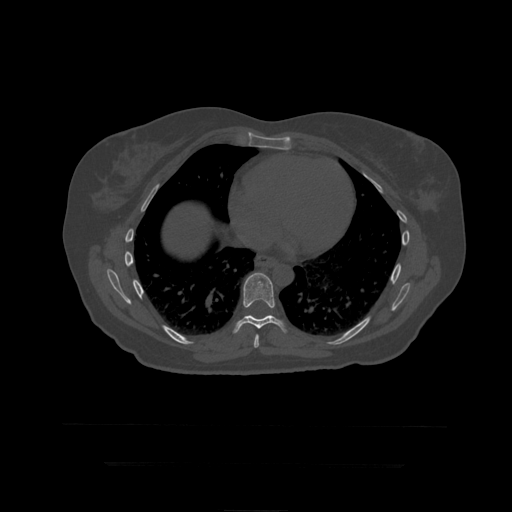
CT including the spine, one axial slice; slice 262 of 399 in the series (ordered by position); reconstruction kernel STANDARD; bone window (W 1800 / L 400 HU); 1.25 mm slice thickness; 512 × 512 image matrix. Patient age 41 years. Case-level facts recorded for this patient, not image findings: primary cancer: breast.
Annotated regions visible in this slice (semi-automatic segmentation, software-assisted and operator-edited):
- T8 vertebra: bounding box [x1, y1, x2, y2] px = [254, 334, 259, 348]
- T9 vertebra: [233, 273, 288, 334]